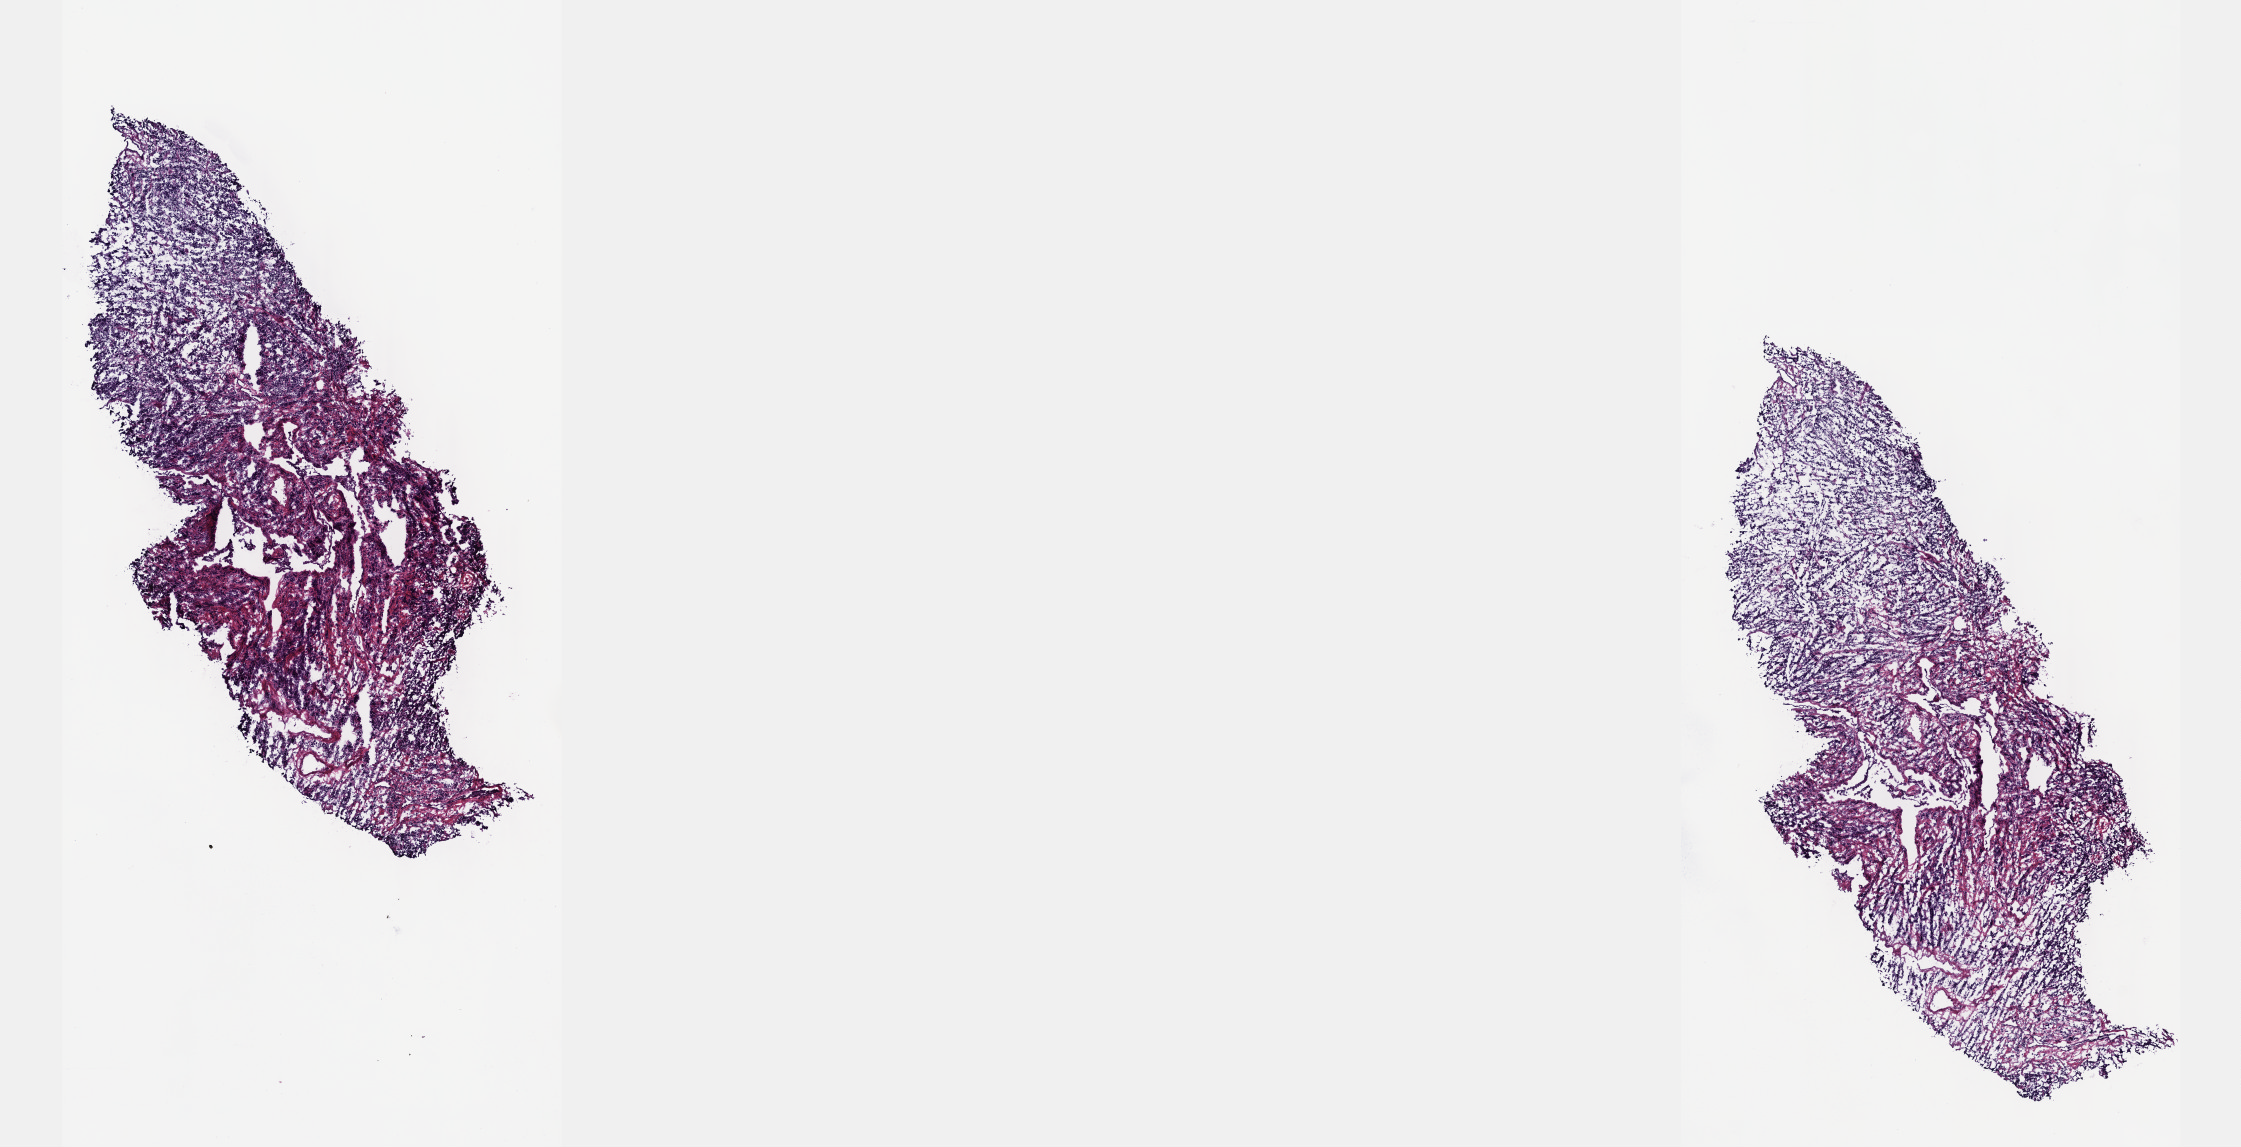
Digitized H&E tissue section (whole slide) — low-resolution overview of the scanned area, about 18.1 x 9.3 mm (slide scanned at 40x), frozen section, primary tumour sample from the testis. Patient: male, age at initial diagnosis 32 years. Composition of this section per pathologist review: tumour cells 100%, tumour nuclei 70%, normal cells 0%, stromal cells 0%, necrosis 0%. Infiltration values recorded for this section: lymphocyte infiltration 1%, monocyte infiltration 0%, neutrophil infiltration 0%.
AJCC pathologic stage: IA (7th edition). Histologic diagnosis: Seminoma, NOS. Laterality: left.